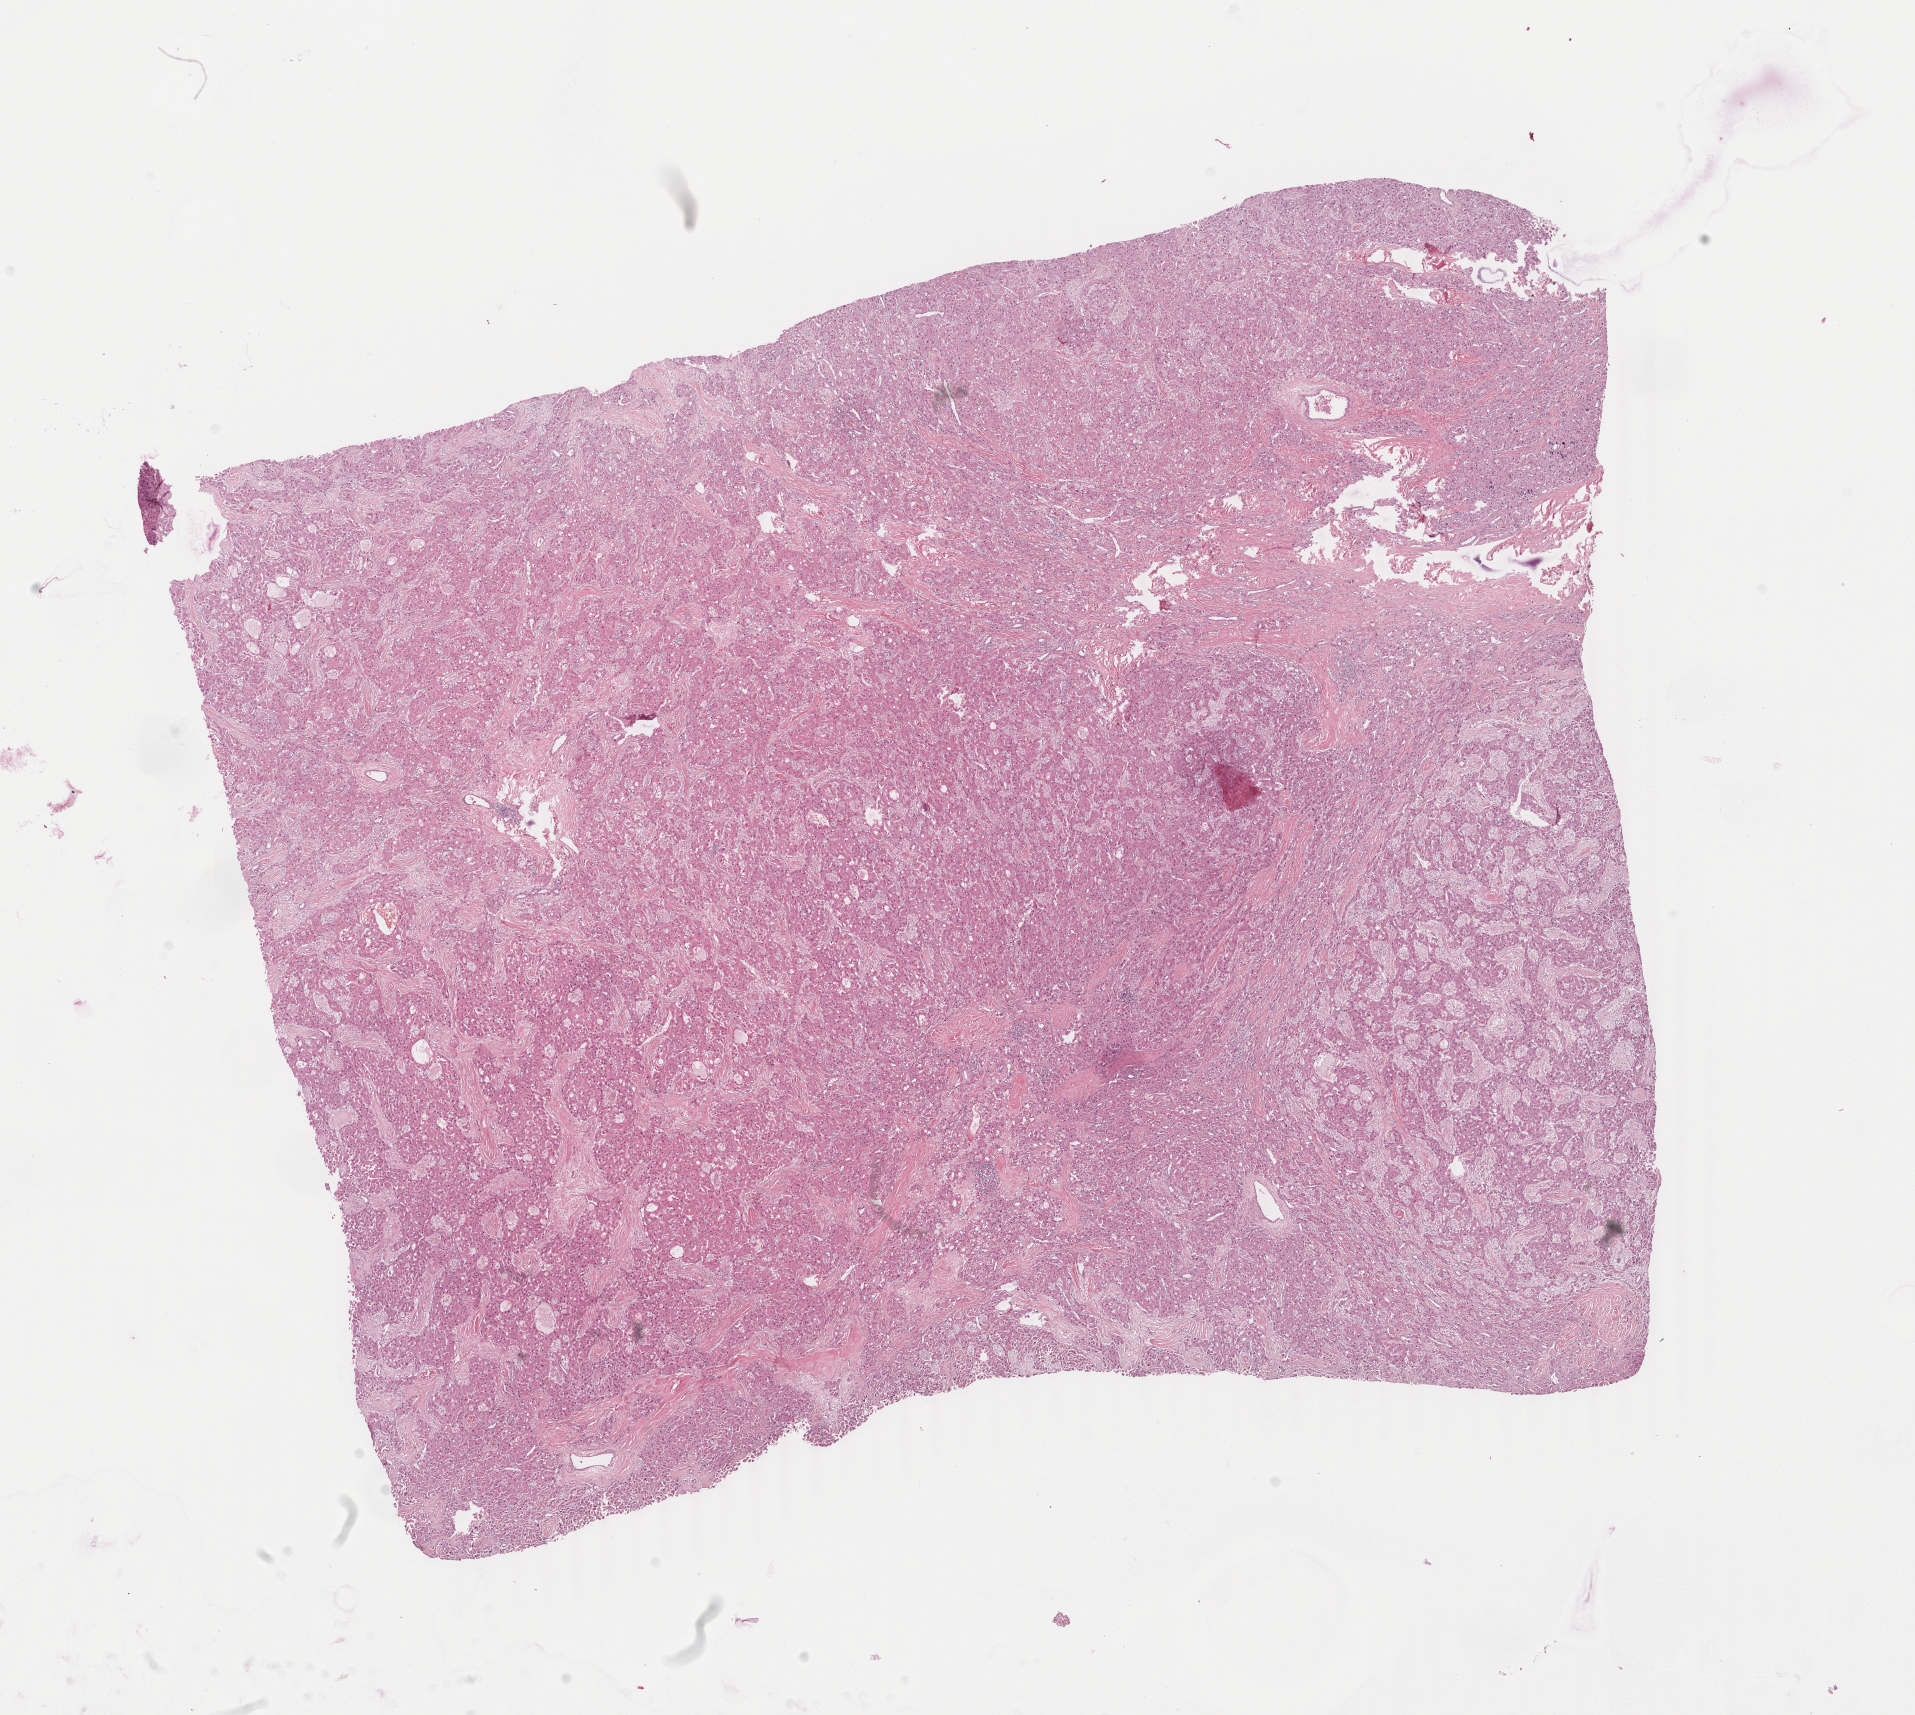
Whole-slide histology image, H&E-stained — low-resolution overview of the scanned area, about 15.2 x 13.6 mm (acquisition: 40x scan), formalin-fixed paraffin-embedded (FFPE) diagnostic section, liver, primary tumour sample. Patient: female, age at initial diagnosis 17 years. Histologic grade: G3 (poorly differentiated).
Histologic diagnosis: Hepatocellular carcinoma, NOS. AJCC pathologic stage: IIIA. TNM: T3a N0 M0.